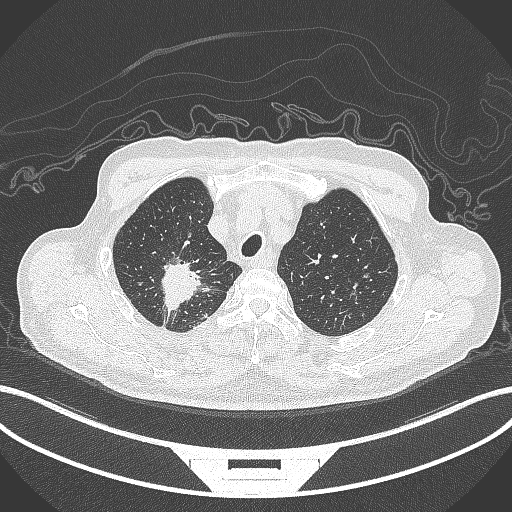
Chest CT, one axial slice; position 315 of 407 along the scan axis; reconstruction kernel B70f; 120 kVp; lung window (W 1500 / L -600 HU); 1 mm slice thickness; 512 × 512 image matrix, field of view 400 × 400 mm. Male patient, age 69 years. Case-level facts recorded for this patient, not image findings: clinical TNM (as recorded): T1c N1 M1.
Outlined on this slice (rectangle marked by the reading radiologist):
- lung tumour (recorded histology: adenocarcinoma): box from (x=154, y=258) to (x=213, y=317) px